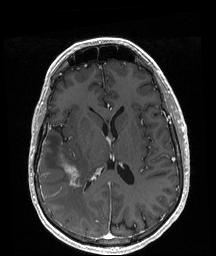
Brain MRI from a brain-tumour surgery series, one axial slice. Position 95 of 208 along the scan axis. T1-weighted post-contrast. 1 mm slice thickness. 216 × 256 image matrix, field of view 211 × 250 mm. From the clinical record (not read from this slice): histopathology: Astrocytoma; WHO grade: 4; IDH mutation: yes.
Structures marked on this image (expert manual segmentation):
- tumour: bounding box [x1, y1, x2, y2] px = [65, 165, 79, 187]